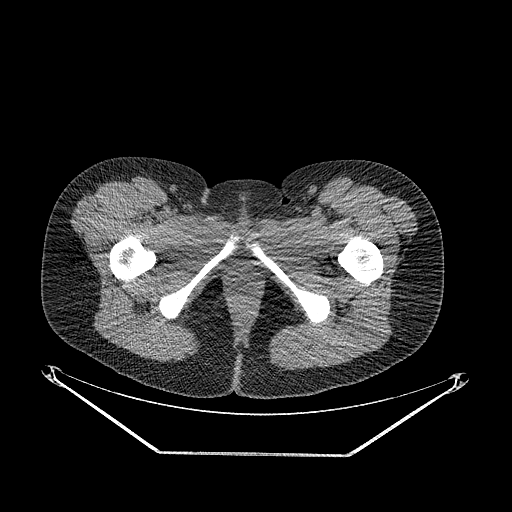
CT of an extremity soft-tissue mass (from a PET/CT study), one axial slice. Slice 35 of 267 in the series (ordered by position). Reconstruction kernel STANDARD. 120 kVp. Soft-tissue window (W 400 / L 40 HU). 3.75 mm slice thickness. 512 × 512 image matrix. Female patient. Case-level facts recorded for this patient, not image findings: histological type: epithelioid sarcoma; grade: intermediate; site of the primary tumour: right buttock.
Annotated regions visible in this slice (expert contour drawn on MRI and transferred to this co-registered scan by the dataset authors):
- gross tumour volume including surrounding oedema: bounding box [x1, y1, x2, y2] px = [183, 297, 218, 339]
- gross tumour volume (mass): [185, 304, 209, 330]